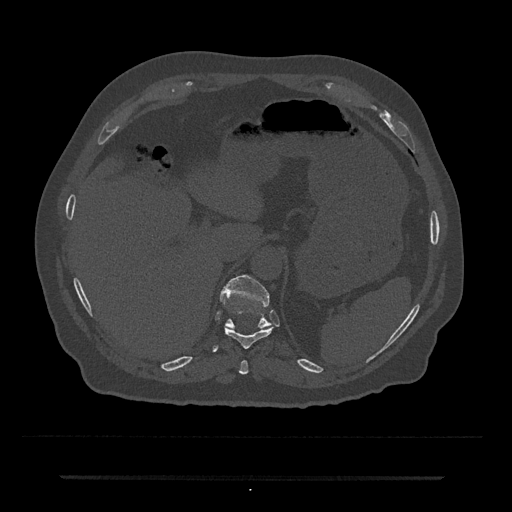
CT including the spine, one axial slice. Position 217 of 797 along the scan axis. Reconstruction kernel Br40s/3. 120 kVp. Bone window (W 1800 / L 400 HU). 0.5 mm slice thickness. 512 × 512 image matrix, field of view 437 × 437 mm. Male patient, age 69 years. Case-level facts recorded for this patient, not image findings: primary cancer: prostate.
Structures marked on this image (semi-automatically segmented with operator editing):
- T10 vertebra: bounding box [x1, y1, x2, y2] px = [212, 311, 274, 352]
- T11 vertebra: [220, 275, 271, 329]
- T9 vertebra: [239, 360, 249, 375]